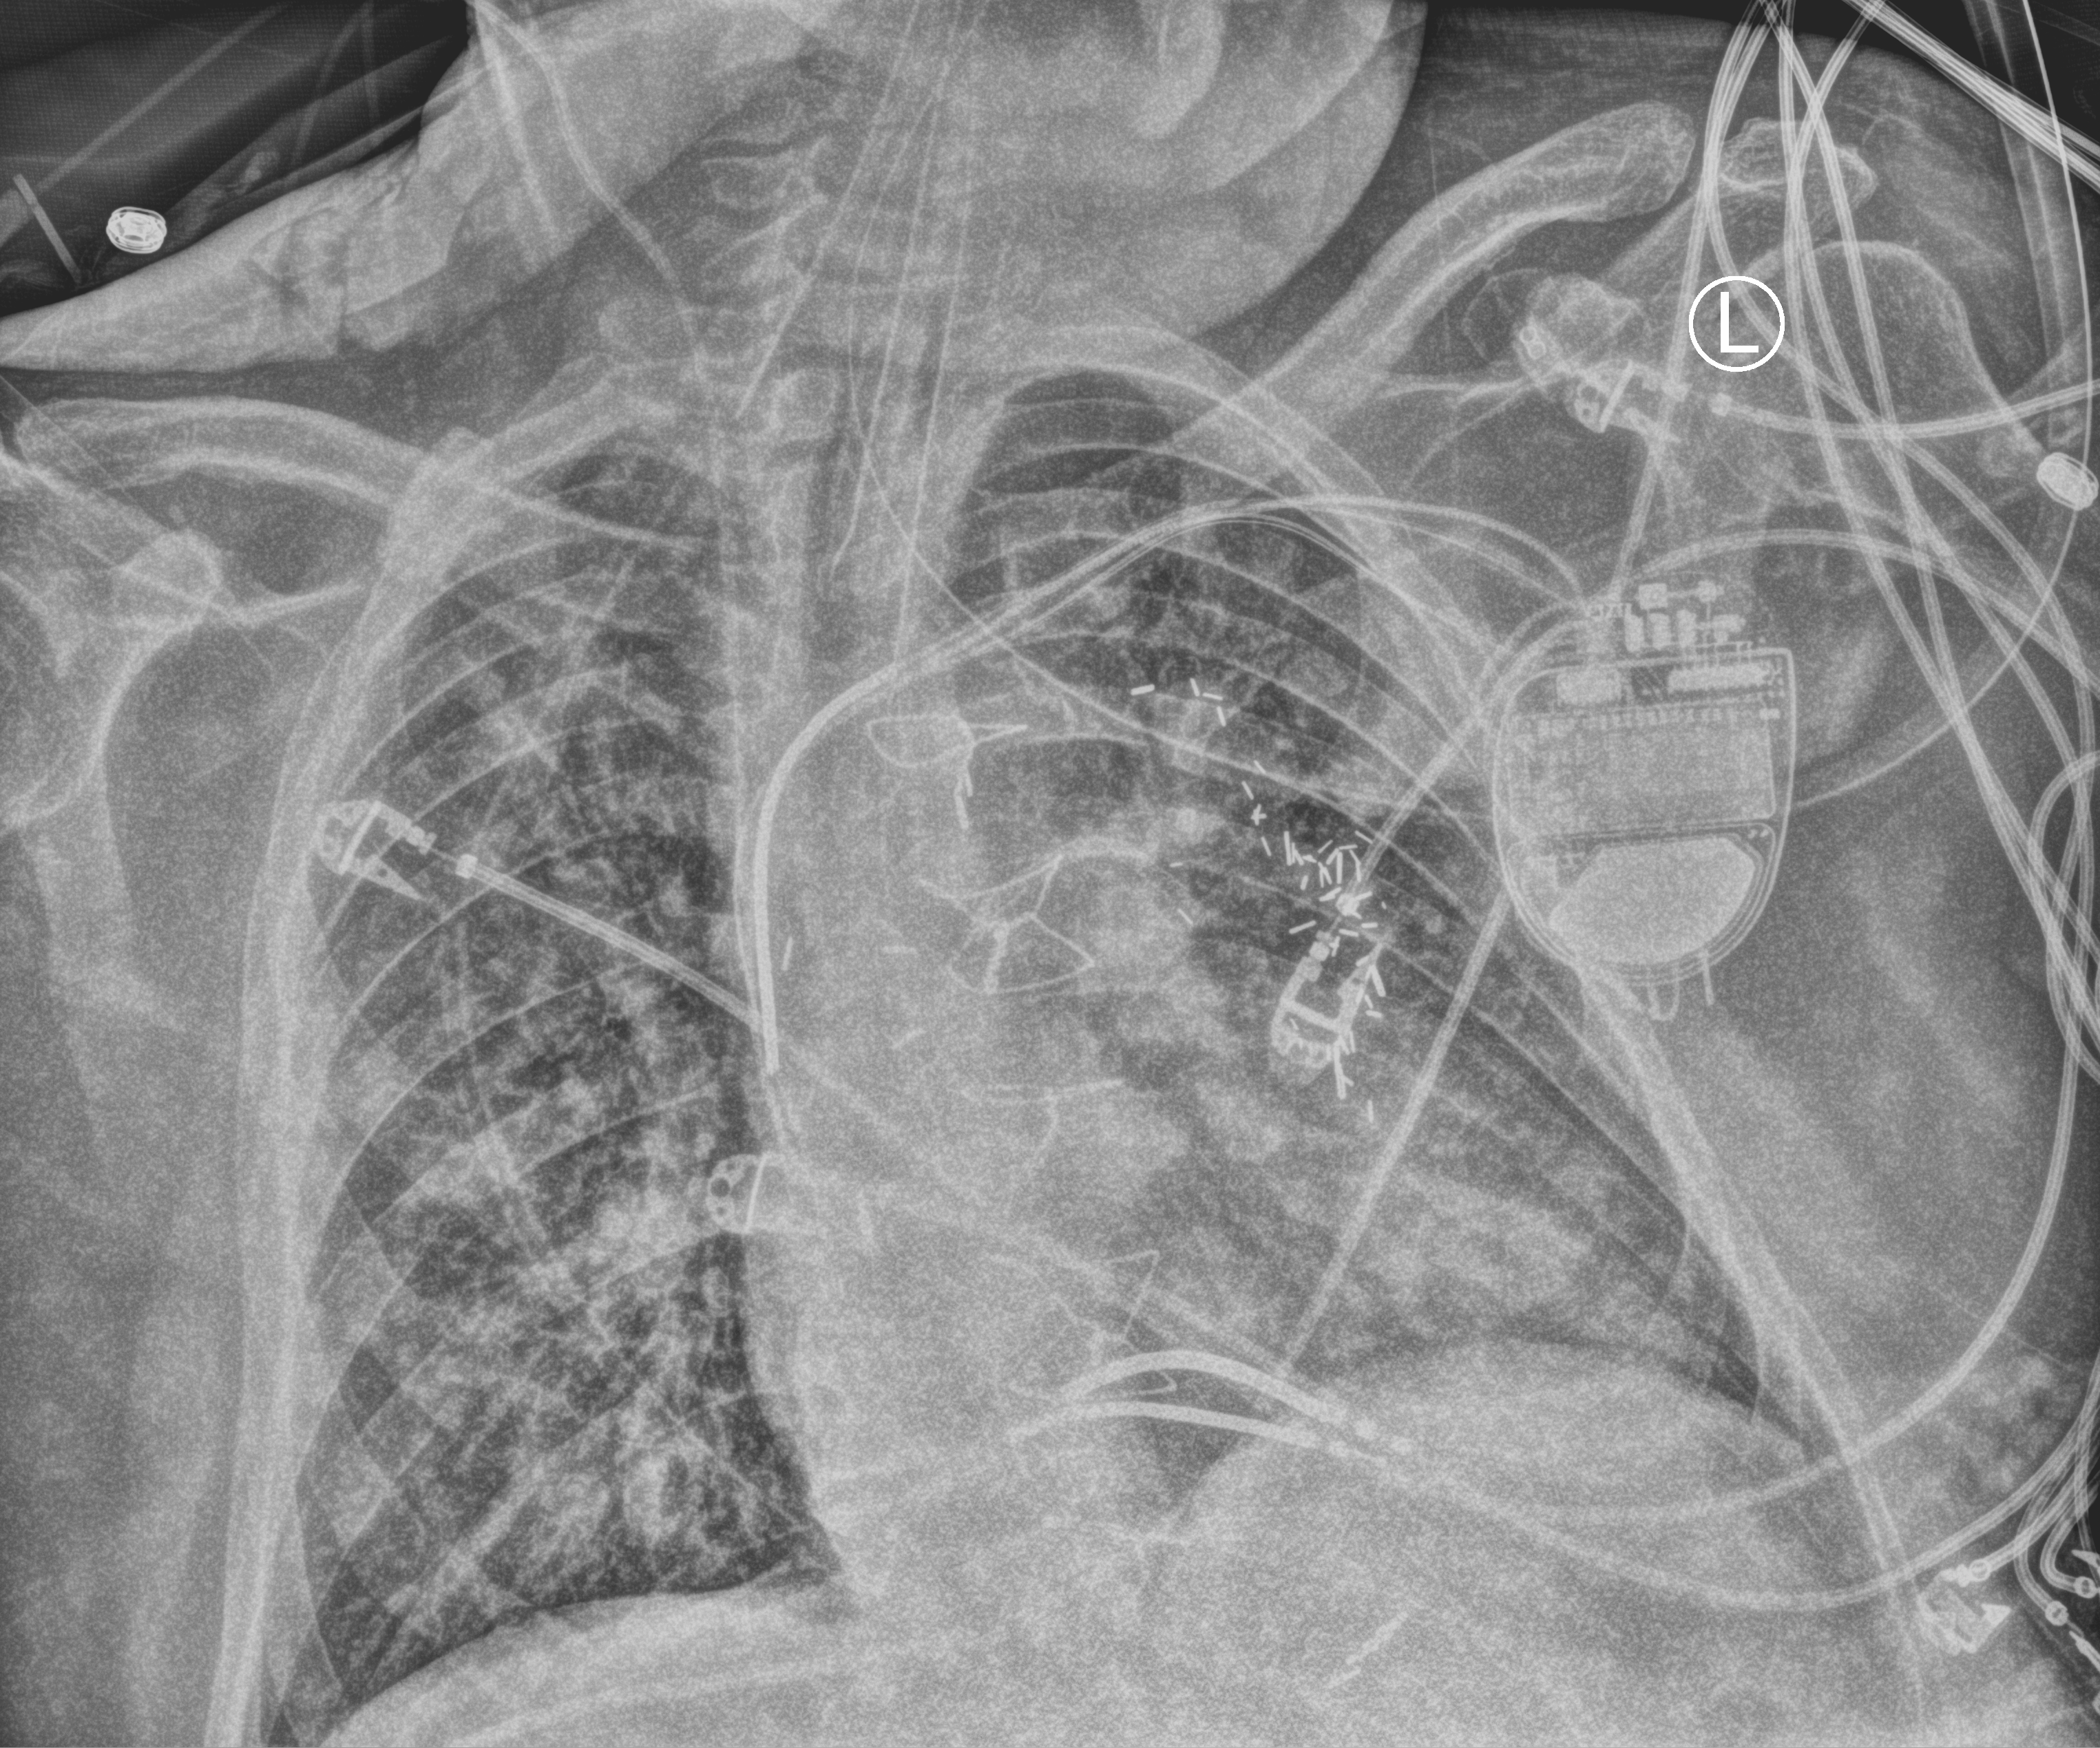
Chest X-ray (portable), anteroposterior (AP) projection. Patient hospitalised with COVID-19; male, aged 60–74 years.
Admission-level facts for this patient (not findings on this image; timing relative to this image not recorded): mechanically ventilated during this hospital stay: yes; COPD (admission record): no.